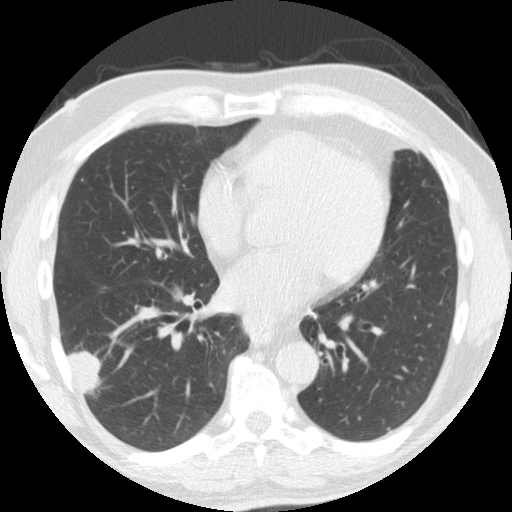
Low-dose screening chest CT, one axial slice; position 76 of 174 along the scan axis; reconstruction kernel STANDARD; lung window (W 1500 / L -600 HU); 2.5 mm slice thickness; 512 × 512 image matrix.
Structures marked on this image (expert manual segmentation):
- lesion 1 (tumor, lower lobe of right lung): bounding box [x1, y1, x2, y2] px = [68, 351, 101, 394]